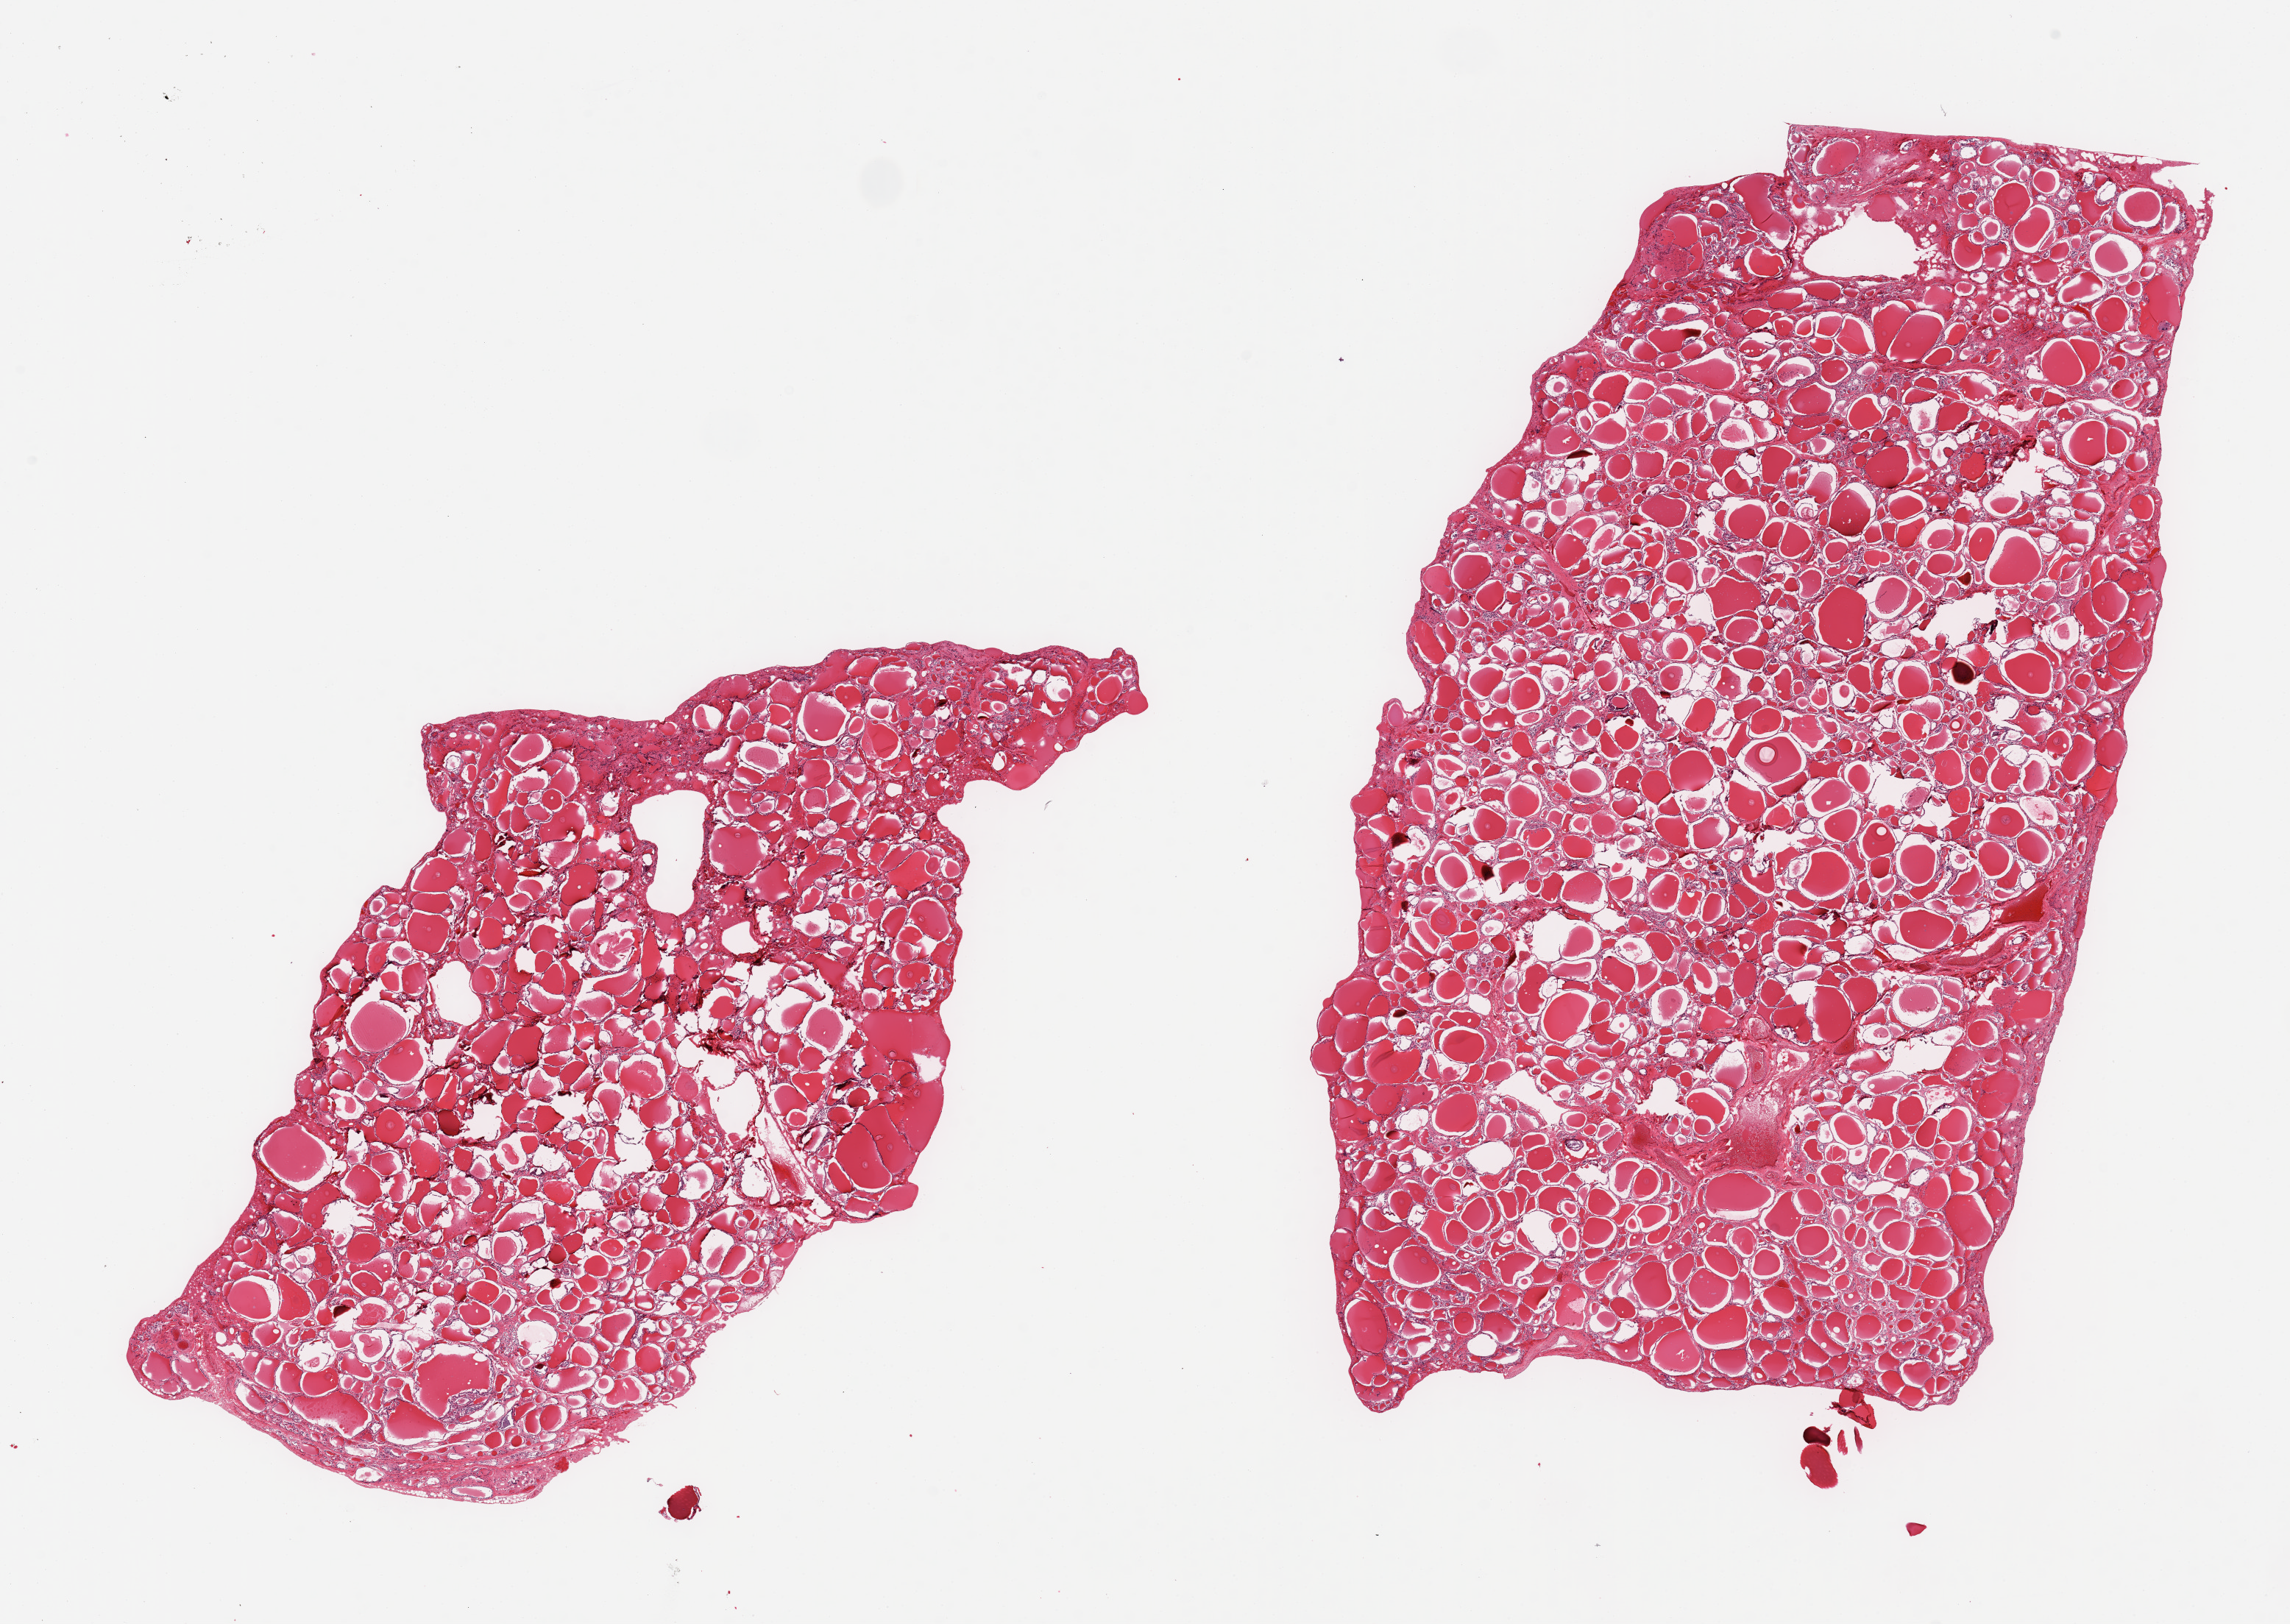
H&E whole-slide image, brightfield, whole scanned area (about 24.6 x 17.5 mm) shown as a low-resolution overview. PAXgene-fixed paraffin-embedded (PFPE) section. Section of thyroid (target tissue). Donor tissue sample. Donor sex: male.
Review note (as recorded): 2 pieces, no abnormalities.